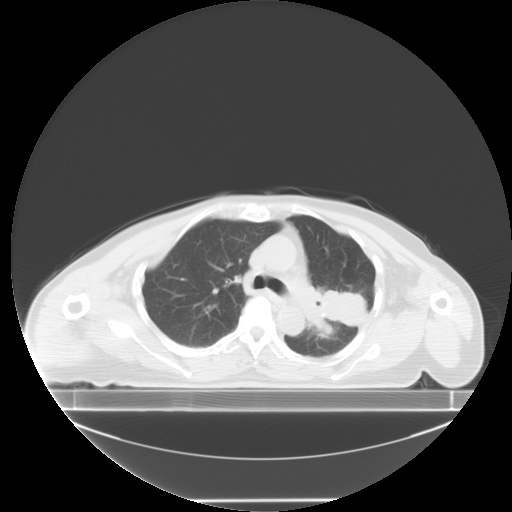
Chest CT, one axial slice; slice 6 of 24 in the series (ordered by position); lung window (W 1500 / L -600 HU); 5 mm slice thickness; 512 × 512 image matrix, field of view 500 × 500 mm. Female patient, age 74 years. Case-level facts recorded for this patient, not image findings: clinical TNM (as recorded): T3 N1 M1c; histopathological grade: G3.
Structures marked on this image (bounding box drawn by a radiologist):
- lung tumour (recorded histology: small cell carcinoma): bounding box <303,277,372,343> (left, top, right, bottom; pixels)